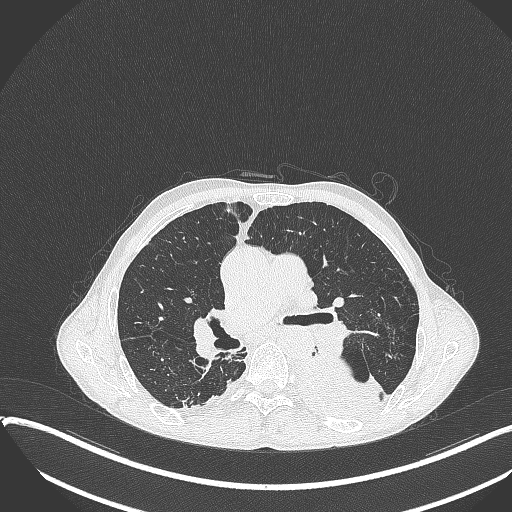
Chest CT, one axial slice; slice 222 of 401 in the series (ordered by position); lung window (W 1500 / L -600 HU); 512 × 512 image matrix, field of view 400 × 400 mm. Male patient, age 57 years. Case-level facts recorded for this patient, not image findings: clinical TNM (as recorded): T4 N0 M0.
Annotated regions visible in this slice (bounding box drawn by a radiologist):
- lung tumour (recorded histology: squamous cell carcinoma): box from (x=298, y=353) to (x=390, y=424) px